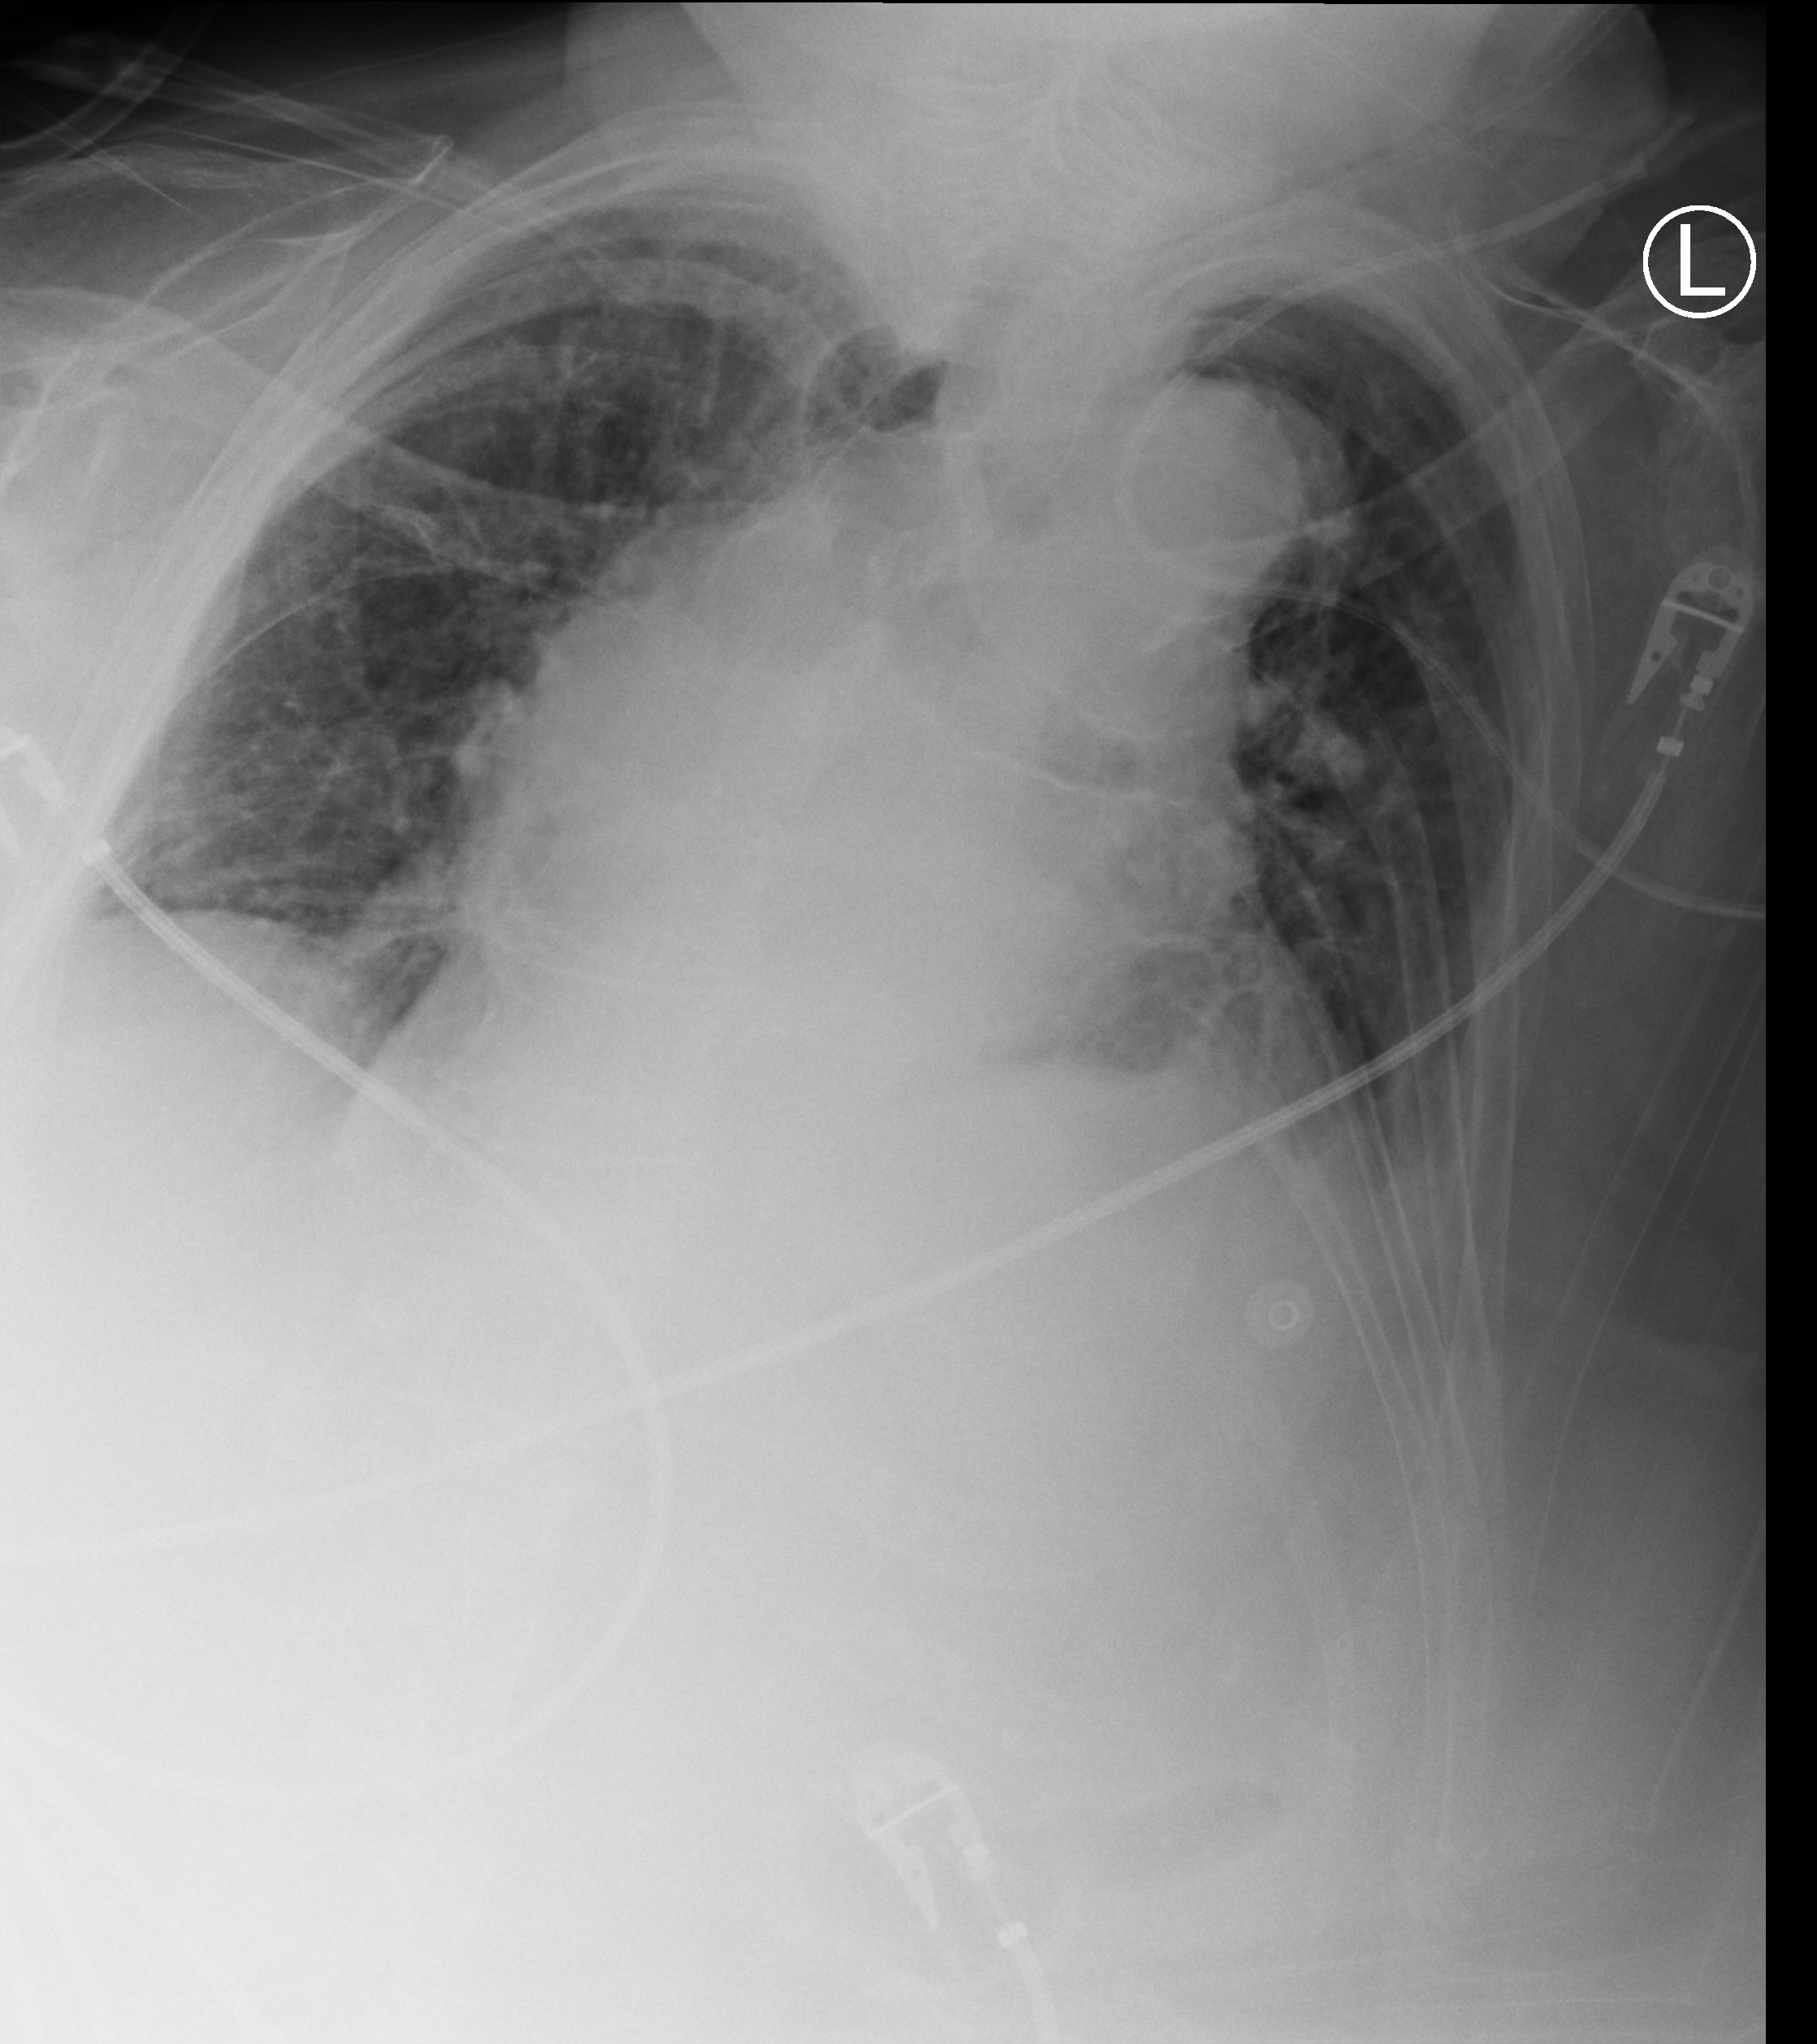
Chest X-ray (portable); anteroposterior (AP) projection. Female patient hospitalised with COVID-19, age 75–90 years.
From the hospital-stay record, not from the radiograph (when in the stay this image was taken is not recorded): mechanically ventilated during this hospital stay: no; admitted to intensive care during this hospital stay: yes.